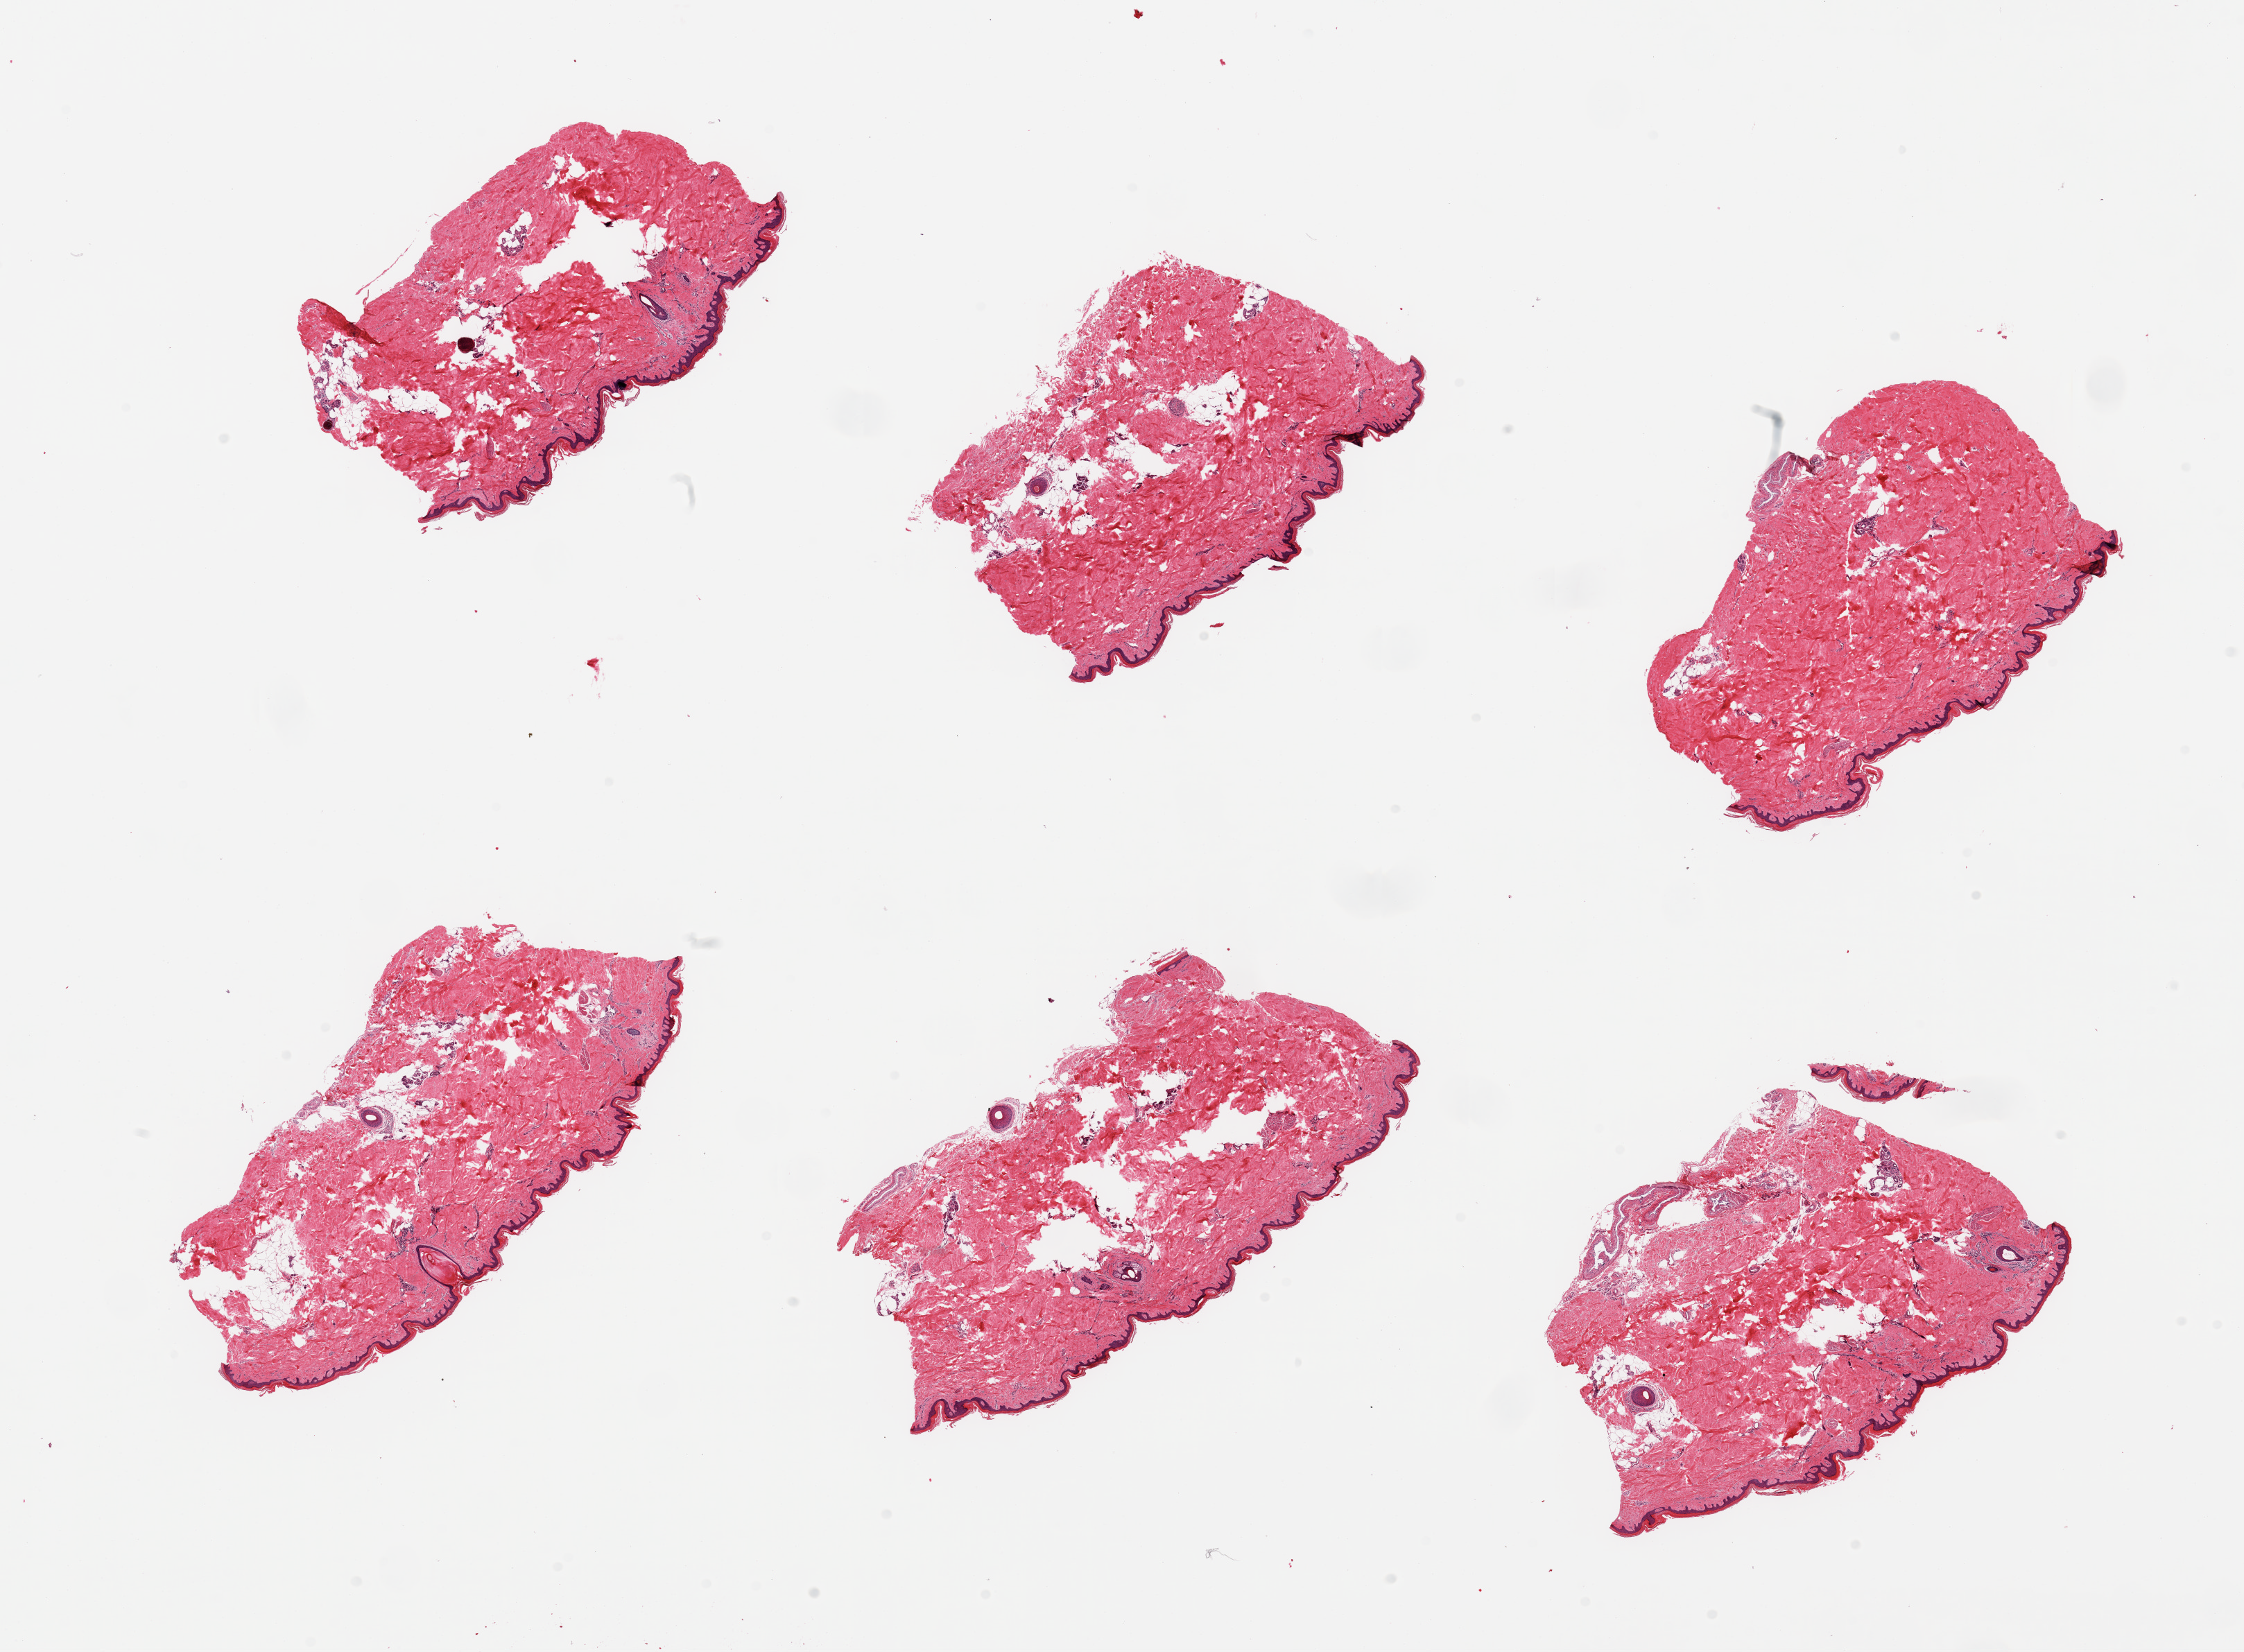
Digitized H&E-stained section — shown as a low-resolution overview of the whole scanned area (about 25.6 x 18.8 mm), PAXgene-fixed, paraffin-embedded tissue, sampled site (target tissue): skin of lower leg, donor tissue sample. Donor: male.
* pathologist's review note for this sample: 6 pieces; ~15% internal fat; epidermis 34.81 um thick